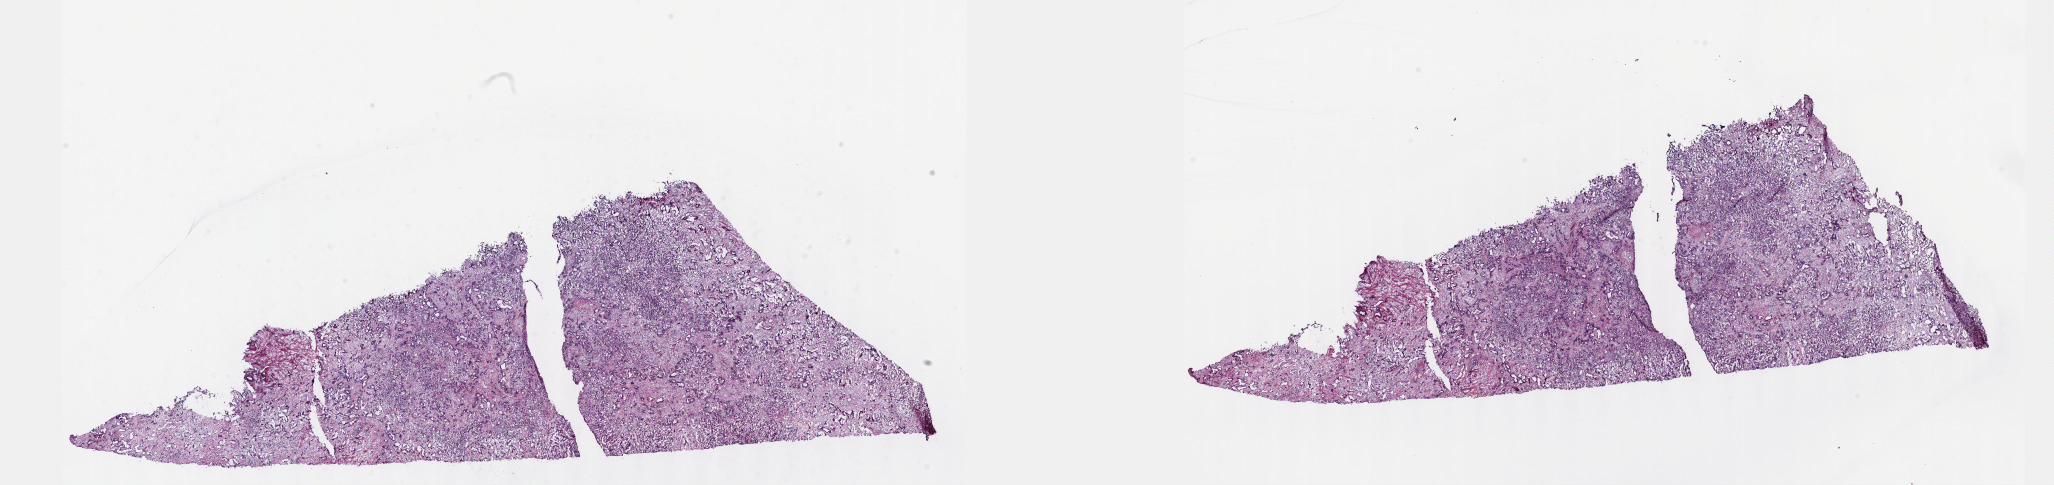
Hematoxylin and eosin (H&E) stained whole-slide image — low-resolution overview of the scanned area, about 33.2 x 7.8 mm (slide scanned at 40x). Frozen section. Sample: primary tumour, liver. Patient: male, age at initial diagnosis 54 years. Histologic grade: G2 (moderately differentiated). Pathologist review of this section (percent, as recorded): tumour cells 50%, tumour nuclei 60%, normal cells 10%, stromal cells 40%, necrosis 0%. Inflammatory infiltration, as recorded: lymphocyte infiltration 0%, monocyte infiltration 0%, neutrophil infiltration 0%.
Pathologic diagnosis: Combined hepatocellular carcinoma and cholangiocarcinoma. AJCC pathologic stage: IIIA (7th edition).